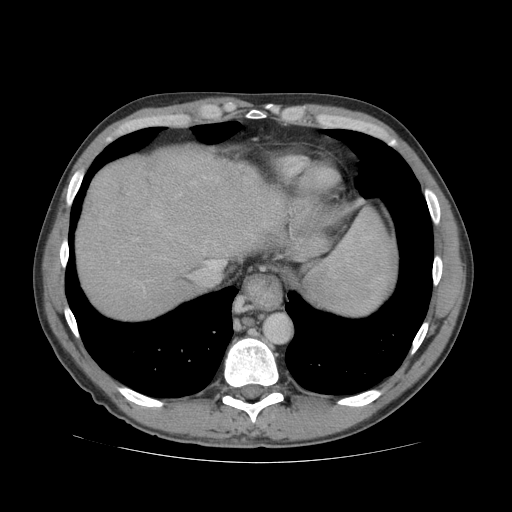
Contrast-enhanced abdominal CT (liver protocol), one axial slice; slice 65 of 81 in the series (ordered by position); reconstruction kernel STANDARD; soft-tissue window (W 400 / L 40 HU); 512 × 512 image matrix. Case-level facts recorded for this patient, not image findings: diagnosis: hepatocellular carcinoma (patient treated with transarterial chemoembolisation; whether this scan precedes or follows treatment is not stated here); TNM stage (as recorded): Stage-IVB; Child-Pugh class: B; tumour differentiation: well differentiated; tumour nodularity: multinodular.
Annotated regions visible in this slice (semi-automatically segmented with operator editing):
- liver parenchyma outside the tumour (the mass and vessels are separate outlines, so this box may not span the whole liver): box from (x=76, y=148) to (x=292, y=318) px
- mass: (x=86, y=156)–(x=152, y=221)
- liver vessels: (x=204, y=177)–(x=224, y=263)